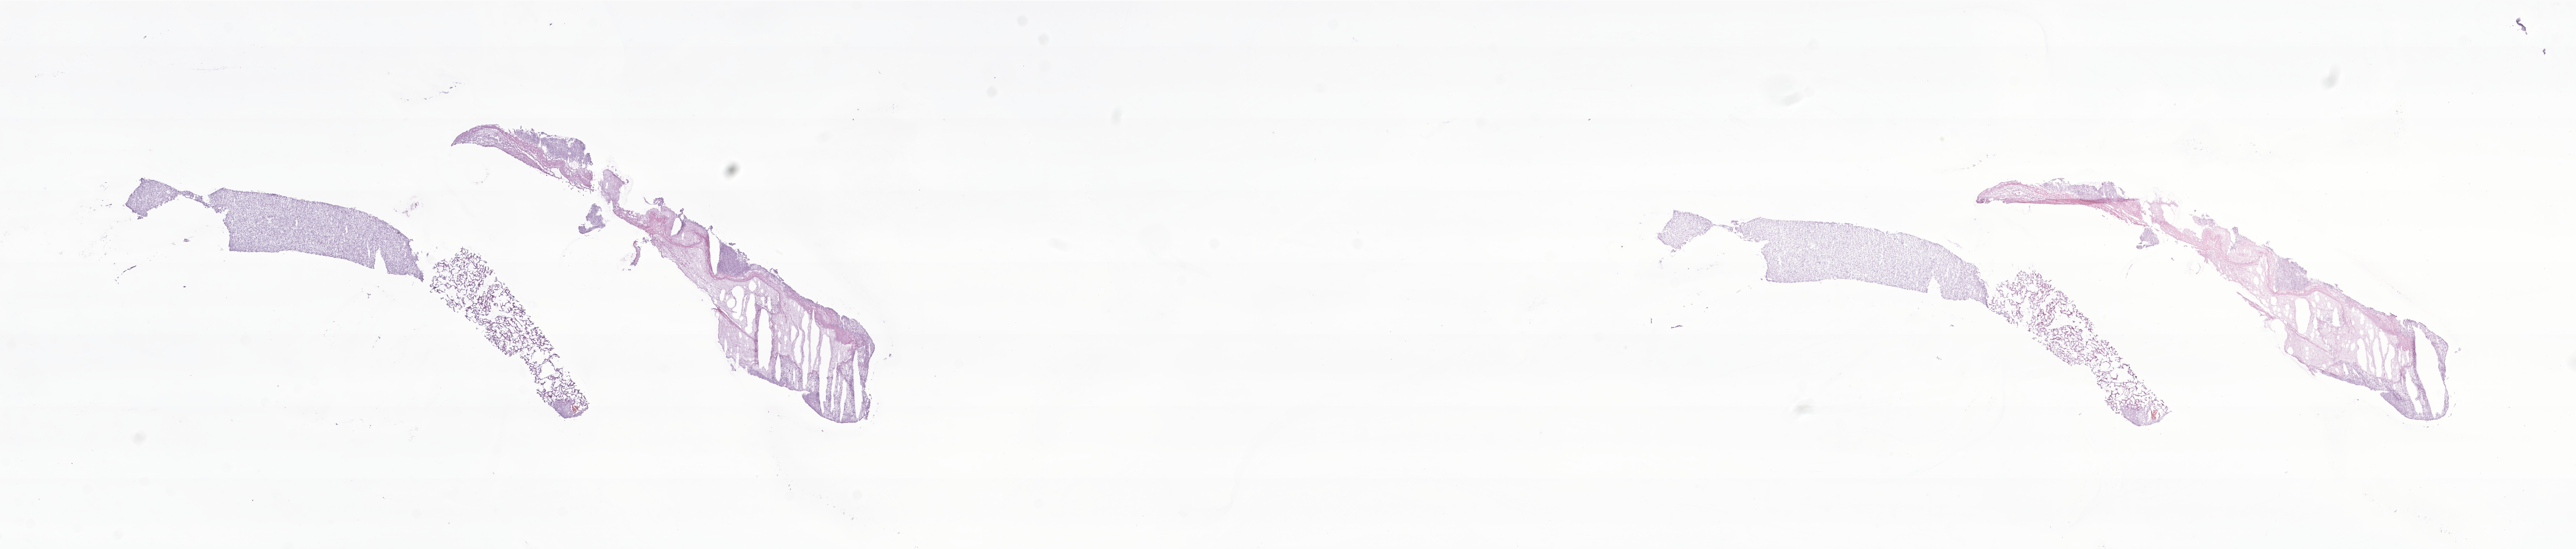
H&E whole-slide image of tumor tissue from the brain — shown as a low-resolution overview of the whole scanned area (about 38.2 x 8.1 mm); frozen section. Female patient, age 214 months (17 years 10 months).
Diagnosis (ICD-O-3 morphology term): Malignant tumor, spindle cell type.